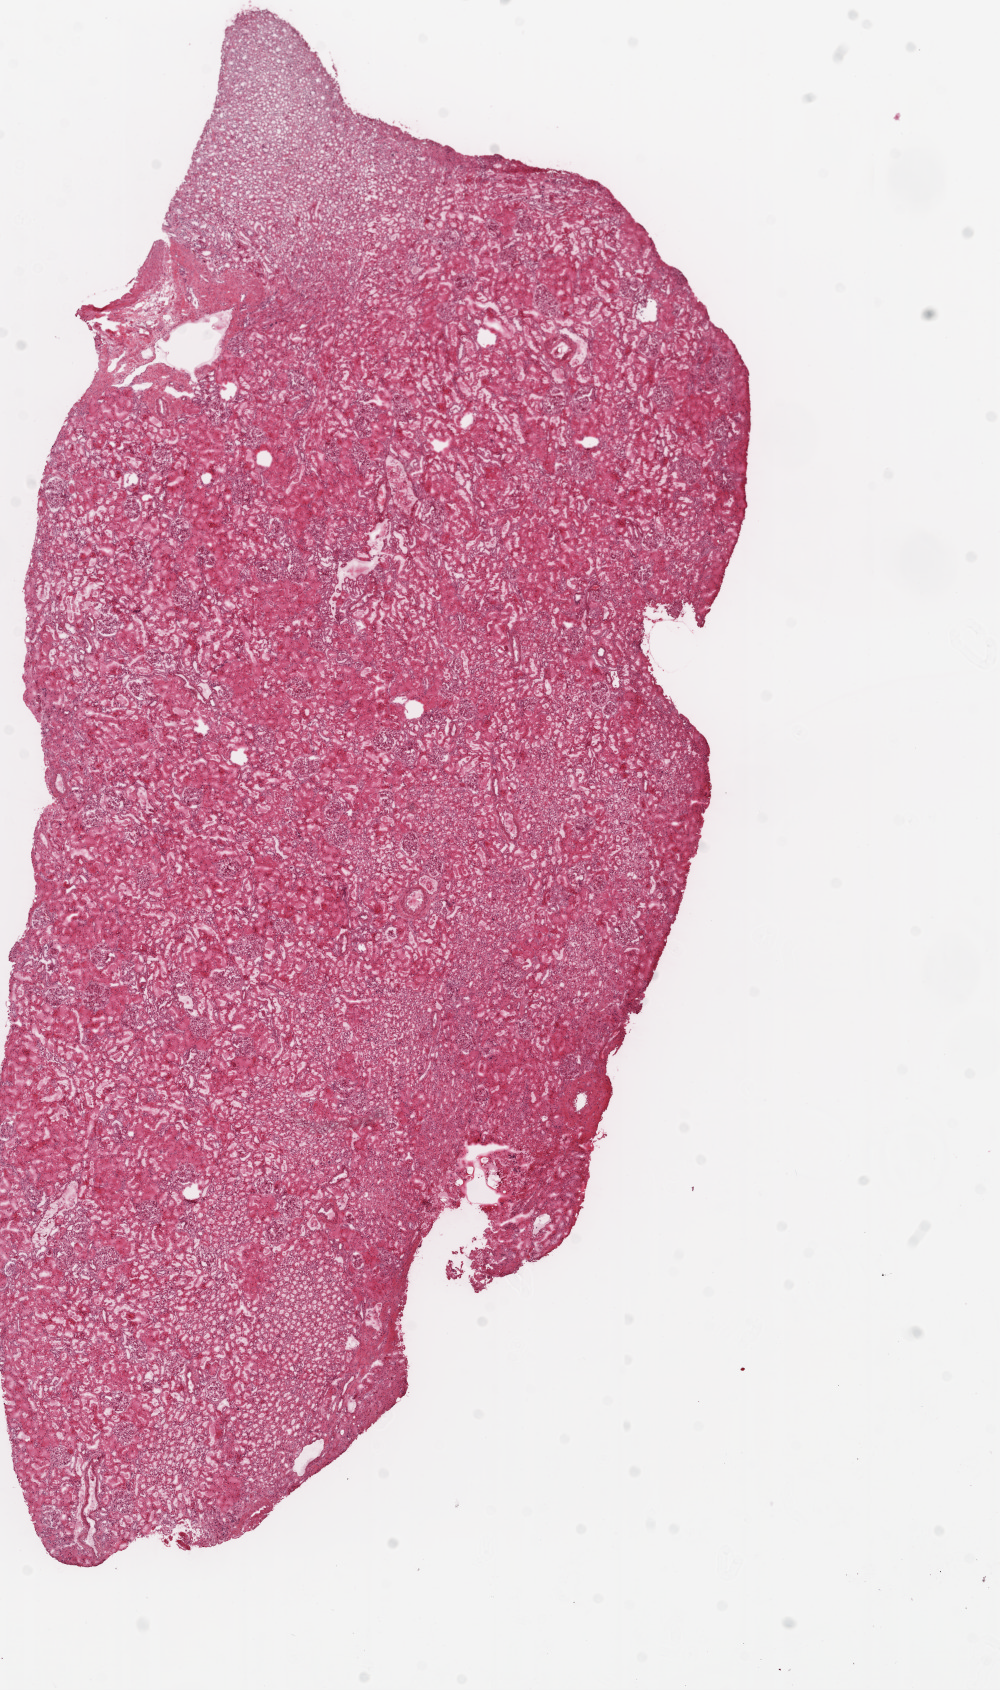
Hematoxylin and eosin (H&E) stained whole-slide image — low-resolution overview of the scanned area, about 8.0 x 13.6 mm (acquisition: 20x scan); frozen section from the top of the tissue portion; solid tissue normal (non-tumour tissue) sample from the kidney. Male, age 46 years at initial diagnosis.
This section: solid tissue normal (non-tumour) sample from the same patient. Patient diagnosis: Clear cell adenocarcinoma, NOS.